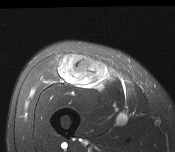
MRI of an extremity soft-tissue mass, one axial slice. Slice 67 of 116 in the series (ordered by position). T2-weighted fat-saturated. MR volume resampled by the dataset authors to the PET/CT grid (not the native acquisition matrix). 3.27 mm slice thickness. 175 × 152 image matrix, field of view 171 × 148 mm. Male patient. From the clinical record (not read from this slice): histological type: pleiomorphic leiomyosarcoma; grade: intermediate; site of the primary tumour: right thigh.
Annotated regions visible in this slice (expert contour drawn on MRI and transferred to this co-registered scan by the dataset authors):
- gross tumour volume including surrounding oedema: bounding box (x1, y1, x2, y2) in pixels: (58, 56, 107, 89)